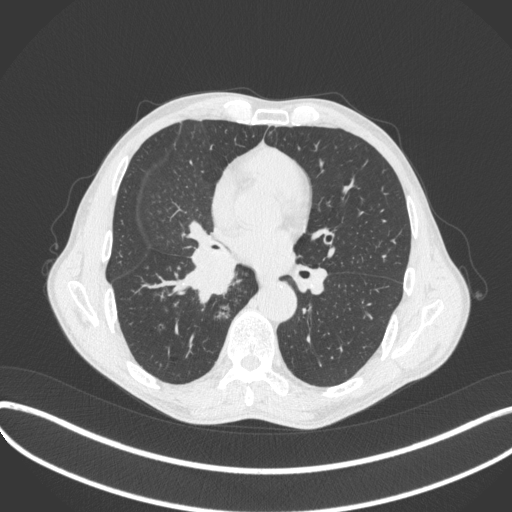
Chest CT, one axial slice. Slice 219 of 481 in the series (ordered by position). Reconstruction kernel B31f. 120 kVp. Lung window (W 1500 / L -600 HU). 1 mm slice thickness. 512 × 512 image matrix. Patient: male, 65 years. Case-level facts recorded for this patient, not image findings: clinical TNM (as recorded): T2a N0 M0.
Annotated regions visible in this slice (bounding box drawn by a radiologist):
- lung tumour (recorded histology: squamous cell carcinoma): bounding box (x1, y1, x2, y2) in pixels: (178, 241, 249, 314)